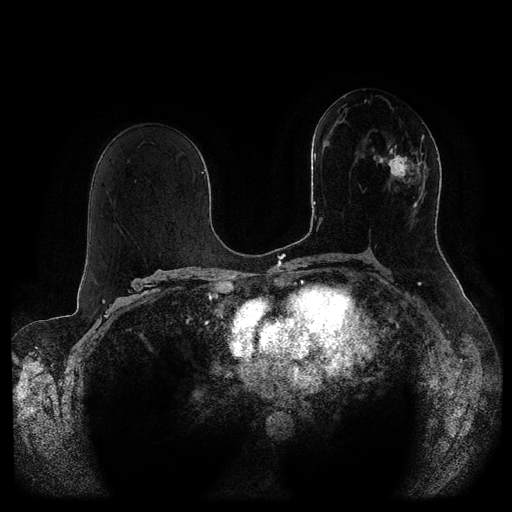
Breast MRI (dynamic contrast-enhanced, multi-phase), one axial slice; slice 53 of 116 in the series (ordered by position); dynamic contrast-enhanced series, time point 2 of 5 at this slice position (early post-contrast); 1.5 T; TE 2.6 ms, TR 5.3 ms; 2 mm slice thickness; 512 × 512 image matrix, field of view 370 × 370 mm. Female patient, age 51 years.
Outlined on this slice (semi-automatically segmented with operator editing):
- breast lesion (labelled 'tumour' in the annotation; benign lesions carry a separate 'benign' label): bounding box [x1, y1, x2, y2] px = [372, 134, 426, 207]